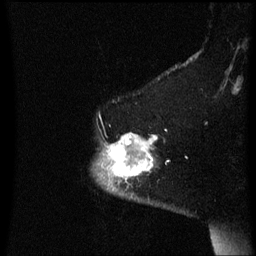
Breast MRI (dynamic contrast-enhanced), one sagittal slice. Position 51 of 60 along the scan axis. Dynamic contrast-enhanced series, image 2 of 3 at this slice position (ordered by acquisition). 1.5 T. TE 4.2 ms, TR 8.4 ms. 256 × 256 image matrix, field of view 200 × 200 mm. Patient: female, 54 years. From the clinical record (not read from this slice): setting: breast cancer imaged before/during neoadjuvant chemotherapy; receptor status: HR-positive, HER2-negative.
Structures marked on this image (semi-automatically segmented with operator editing):
- analysis volume of interest (the breast-tissue region the enhancement analysis was run in; not a lesion): box from (x=95, y=134) to (x=159, y=191) px
- tumour enhancement mask (voxels above the 70 % enhancement threshold inside the analysis volume of interest): (x=107, y=134)–(x=159, y=183)